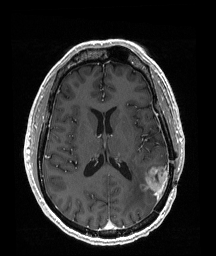
Brain MRI from a brain-tumour surgery series, one axial slice; position 84 of 192 along the scan axis; T1-weighted post-contrast; 1 mm slice thickness; 216 × 256 image matrix. Case-level facts recorded for this patient, not image findings: histopathology: Glioblastoma; WHO grade: 4; IDH mutation: no; tumour location: Left Temporoparietal.
Structures marked on this image (expert manual segmentation):
- tumour: box from (x=144, y=166) to (x=170, y=197) px